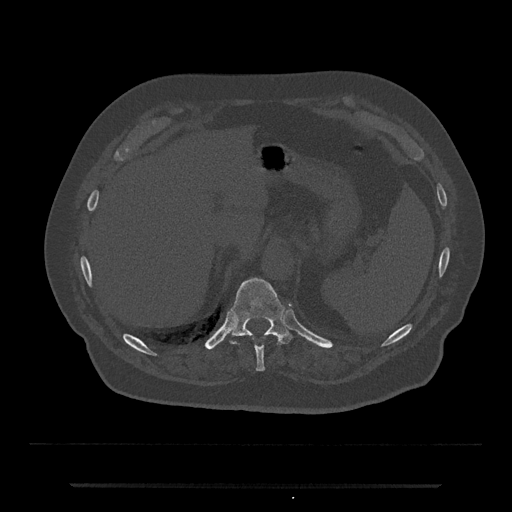
CT including the spine, one axial slice; slice 668 of 797 in the series (ordered by position); reconstruction kernel Br40s/3; bone window (W 1800 / L 400 HU); 512 × 512 image matrix, field of view 434 × 434 mm. Patient: male, 80 years. Case-level facts recorded for this patient, not image findings: primary cancer: prostate; vertebrae with lytic lesions (as recorded): L1, T11.
Annotated regions visible in this slice (semi-automatically segmented with operator editing):
- T10 vertebra: bounding box [x1, y1, x2, y2] px = [255, 346, 265, 371]
- T11 vertebra: [229, 278, 294, 345]